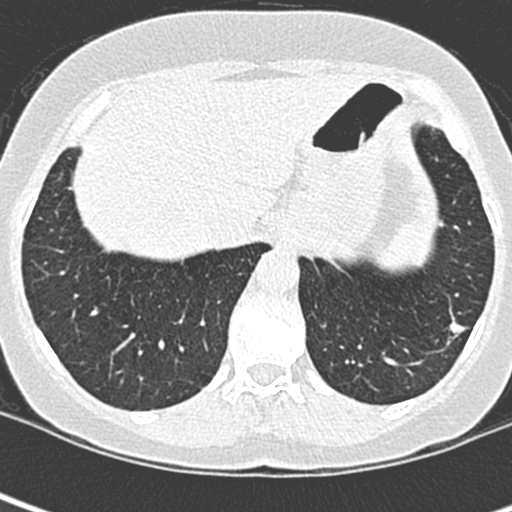
Low-dose screening chest CT, one axial slice; slice 58 of 252 in the series (ordered by position); 120 kVp; lung window (W 1500 / L -600 HU); 1.3 mm slice thickness; 512 × 512 image matrix.
Annotated regions visible in this slice (outlined manually by an expert reader):
- lesion 1 (tumor, lower lobe of left lung): bounding box [x1, y1, x2, y2] px = [449, 320, 468, 336]